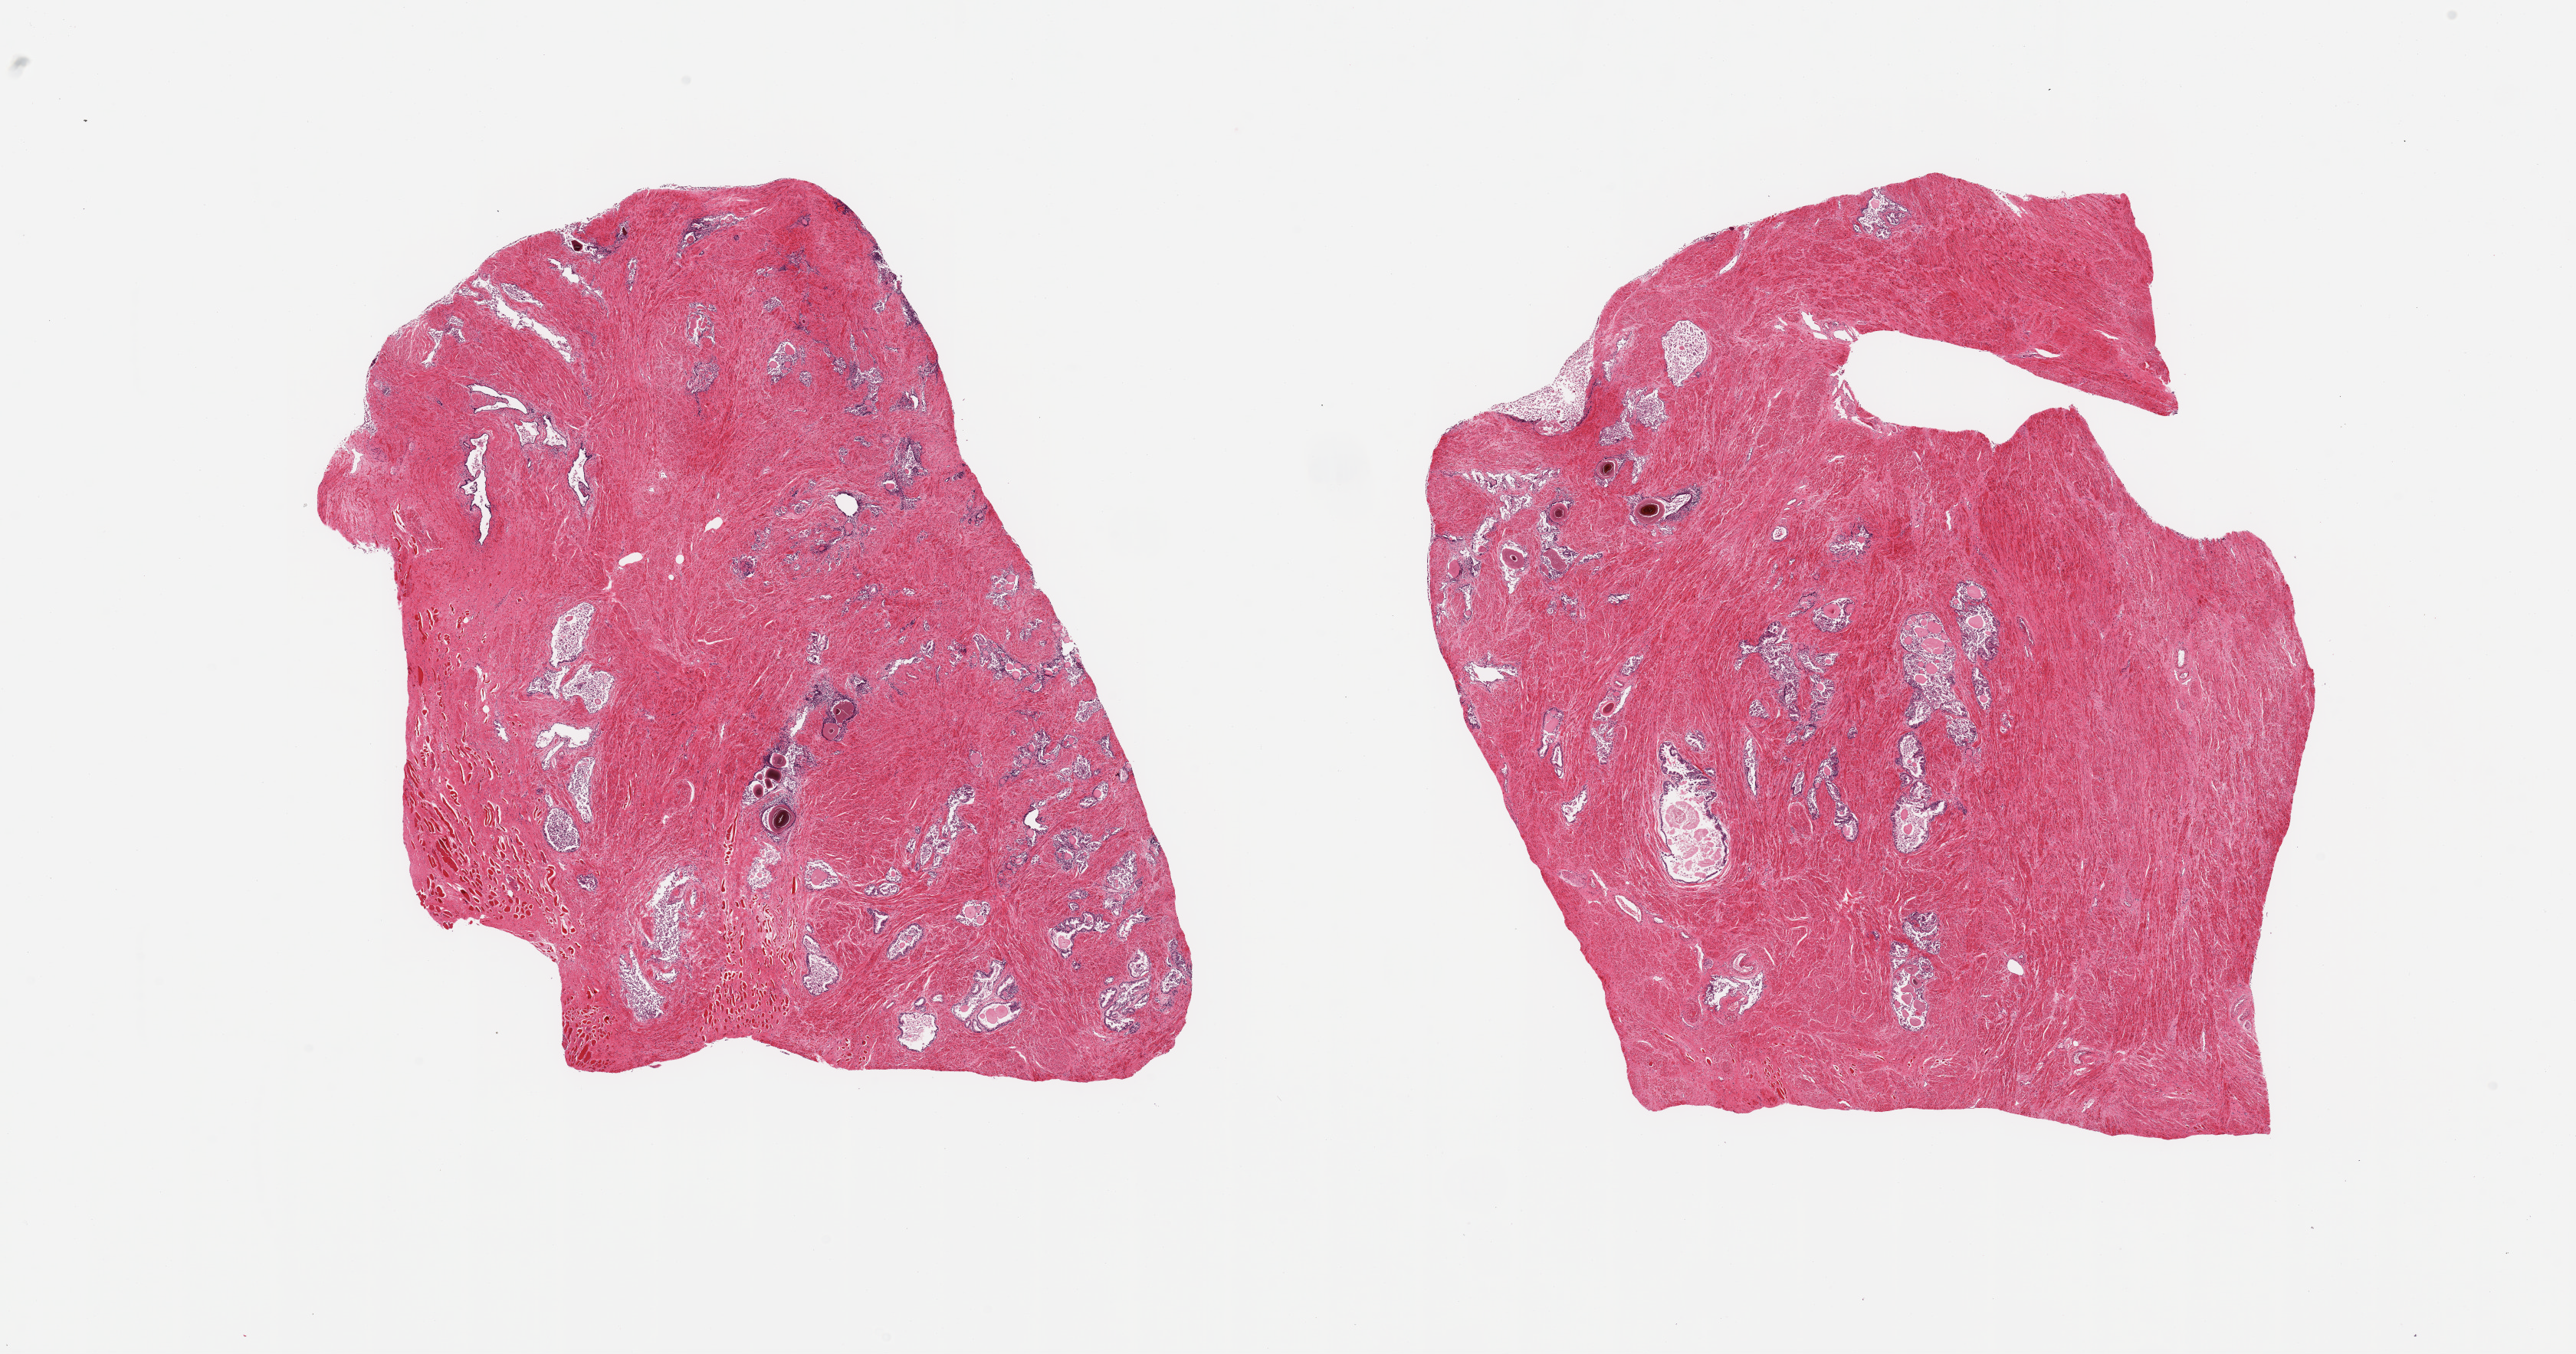
Whole-slide image, haematoxylin and eosin stain, low-resolution overview of the scanned area, about 26.6 x 14.0 mm, PAXgene-fixed, paraffin-embedded tissue, target tissue: prostate, tissue donor sample. Male donor.
* reviewer comment on this tissue sample: 2 pieces; glands severely [3] autolyzed, stroma preserved [1]; scattered skeletal muscle fibers on periphery of both pieces